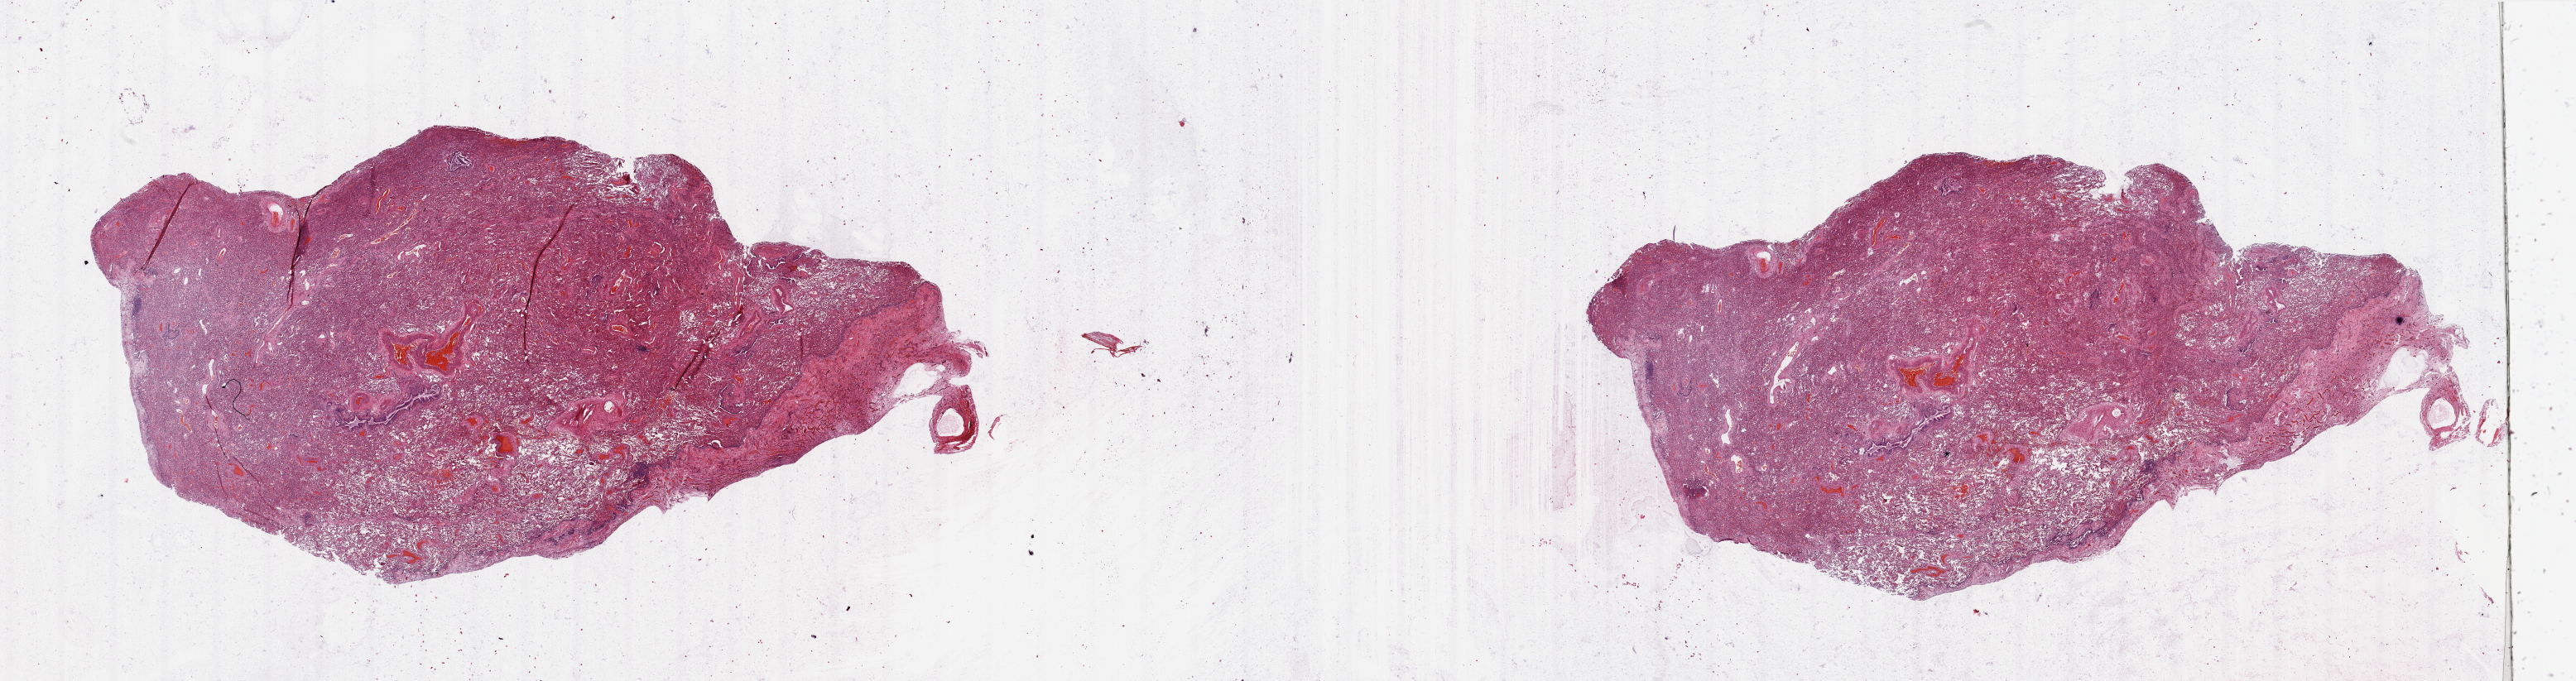
Digitized H&E tissue section (whole slide), whole scanned area (about 49.2 x 13.0 mm, slide scanned at 20x) shown as a low-resolution overview. Normal (non-tumour) tissue sample, lung. Male, 72 y/o.
This section: normal (non-tumour) tissue from the same patient. Patient diagnosis: Squamous cell carcinoma, NOS.